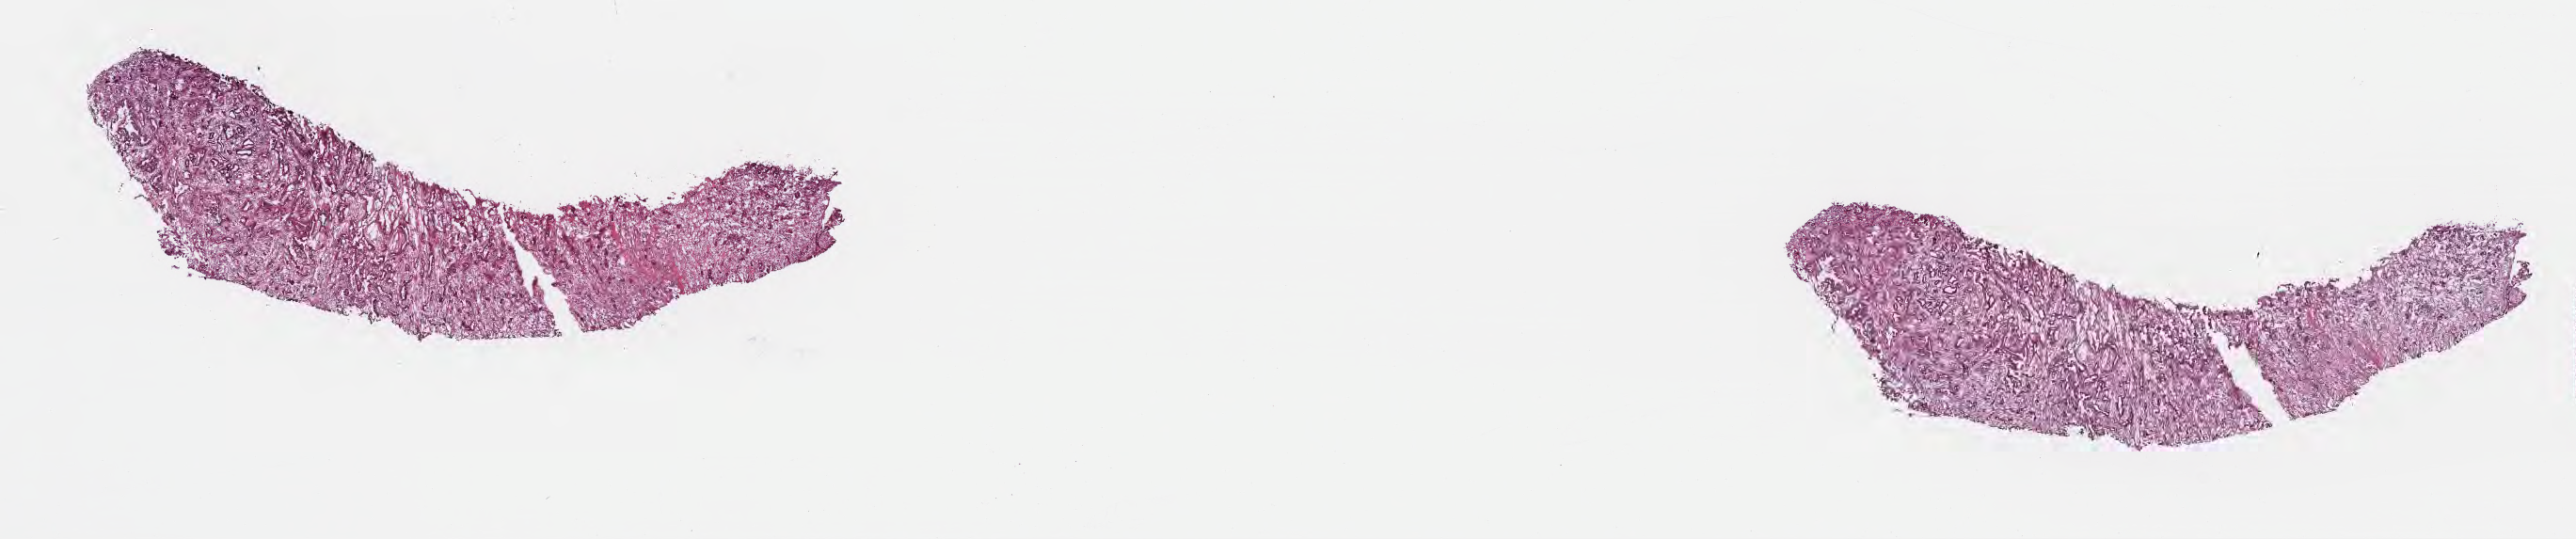
Digitized H&E-stained section — whole scanned area (about 22.1 x 4.6 mm) shown as a low-resolution overview, frozen section (tissue freezing medium), primary tumor, anatomic site: head of pancreas. Male, age 74 years at initial diagnosis. Composition of this section per pathologist review: tumor cells 70%, tumor nuclei 80%, stromal cells 30%, necrosis 0%, normal cells 0%. Inflammatory infiltration, as recorded: lymphocyte infiltration 0%, monocyte infiltration 0%, neutrophil infiltration 0%.
Diagnosis: Intraductal papillary mucinous neoplasm with invasive carcinoma. AJCC pathologic stage: Stage III.